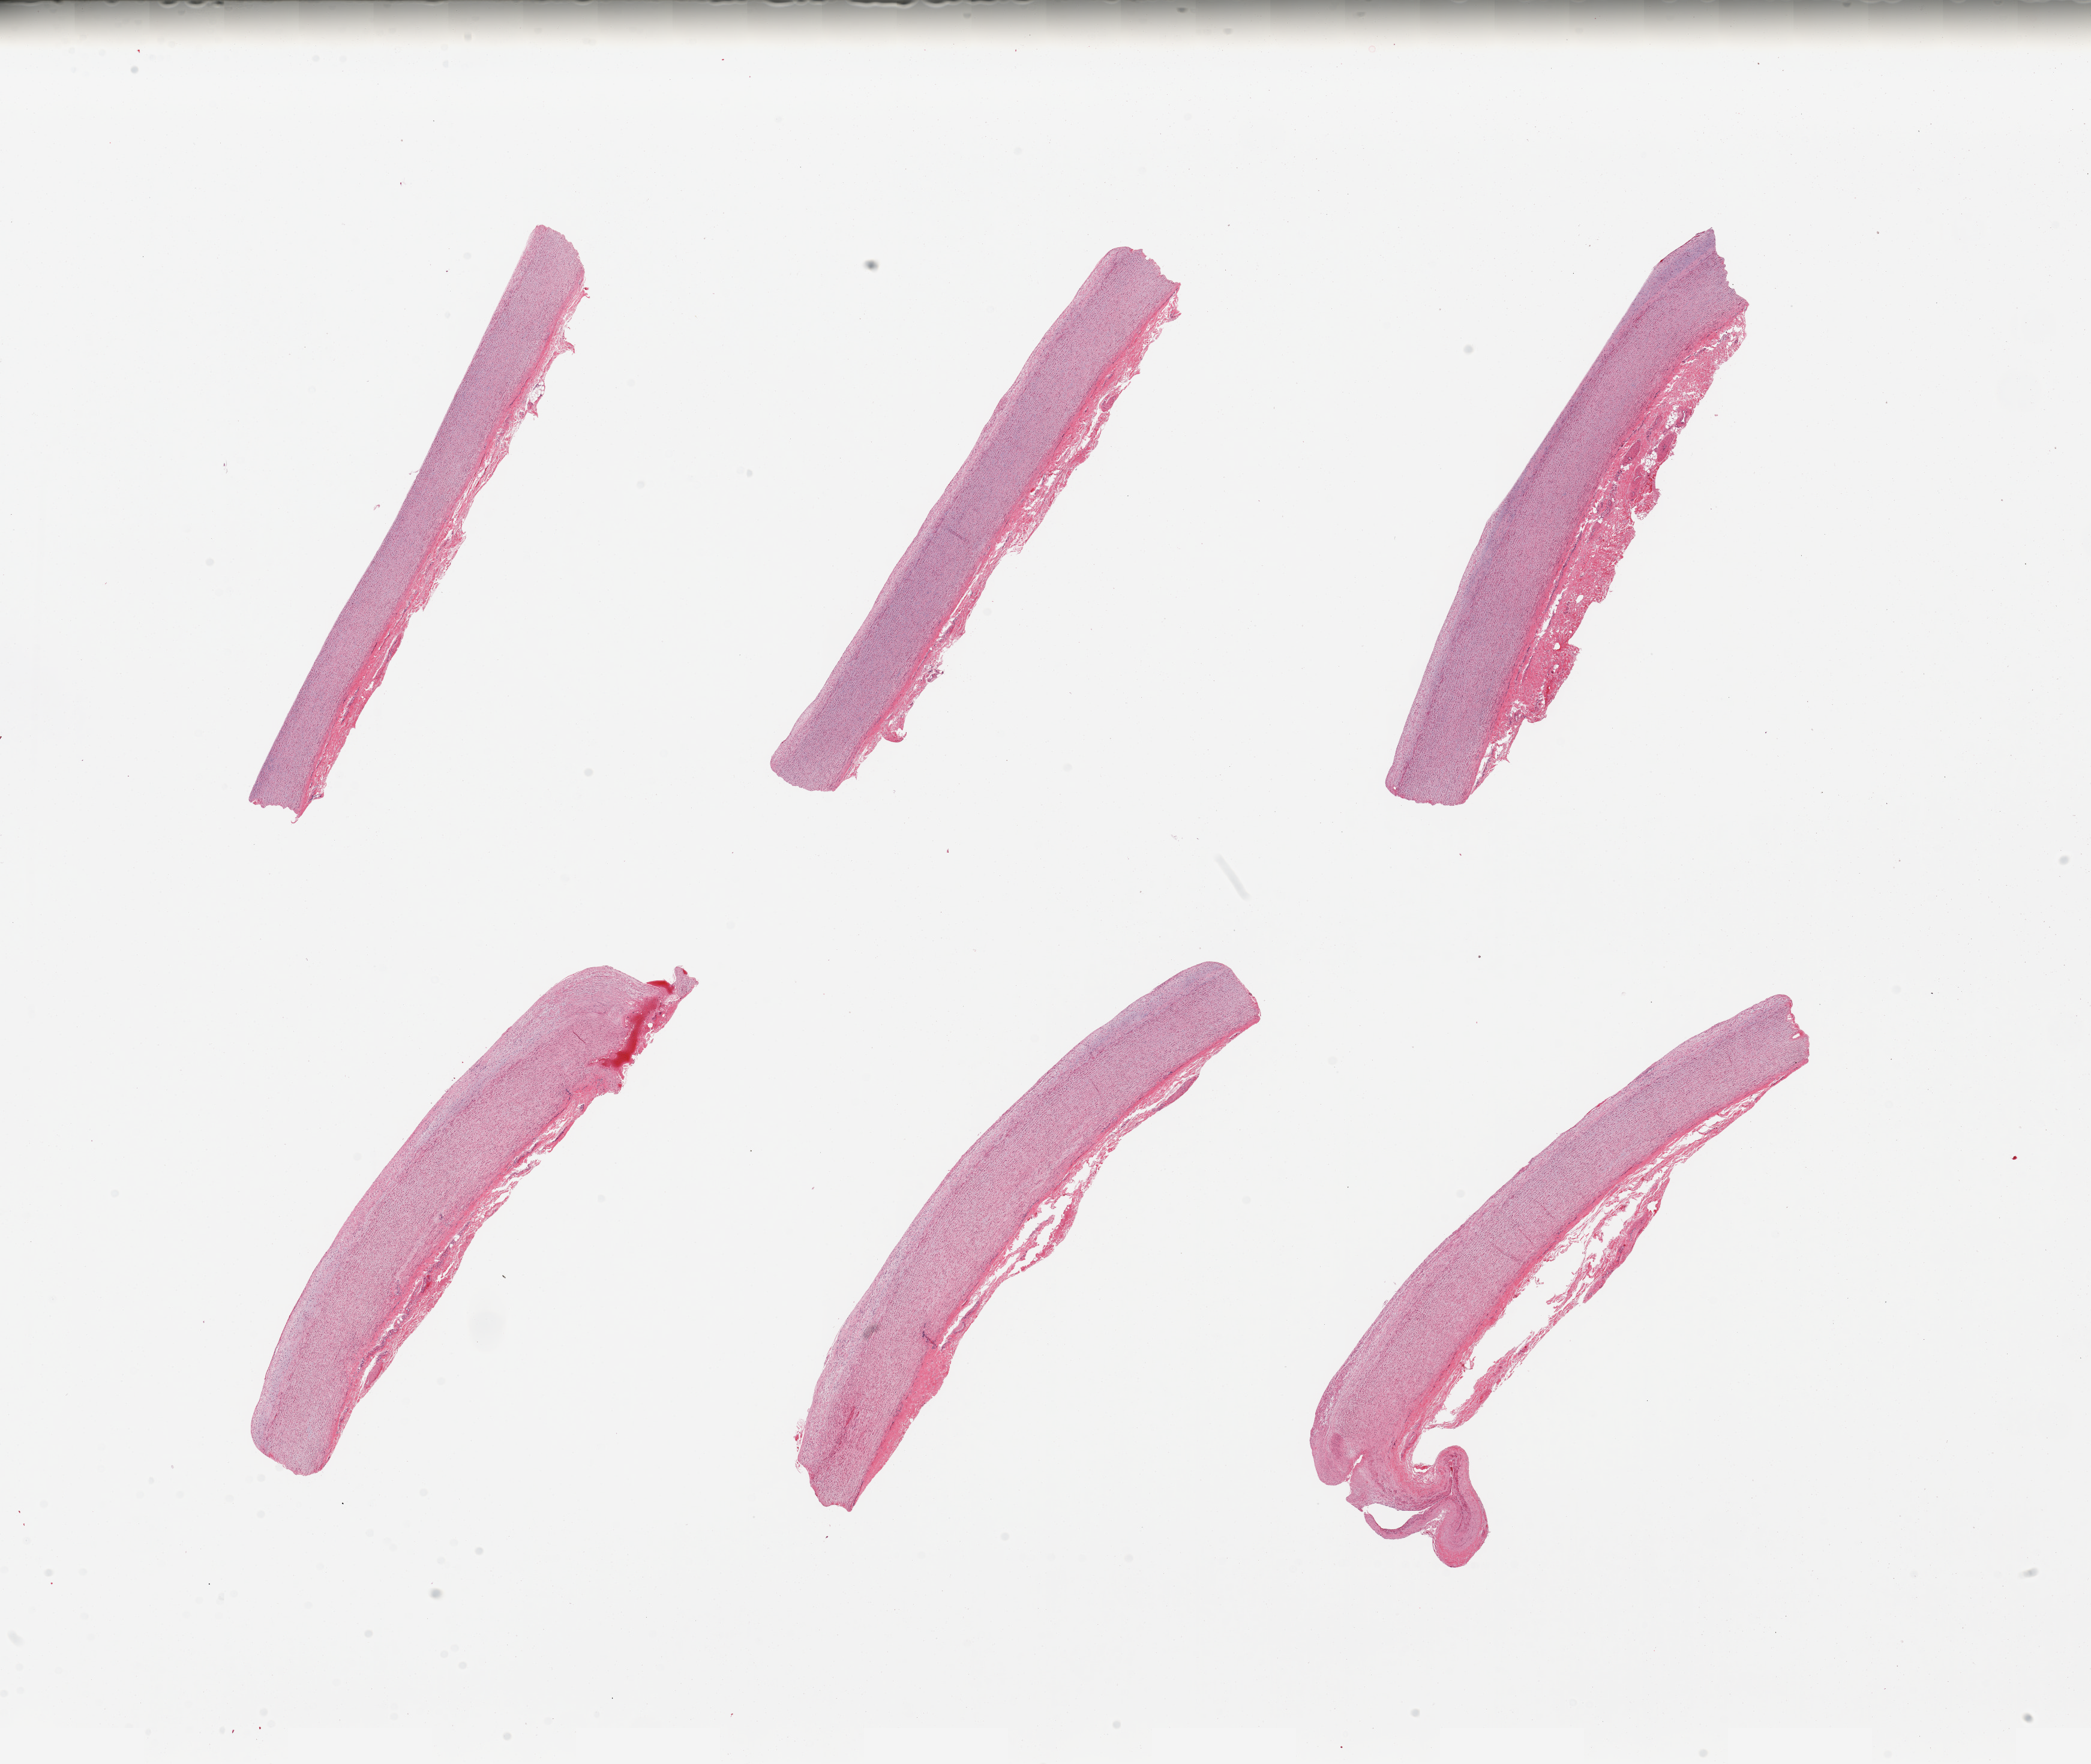
Hematoxylin and eosin (H&E) whole-slide image — shown as a low-resolution overview of the whole scanned area (about 27.6 x 23.3 mm); PAXgene-fixed, paraffin-embedded tissue; target tissue: aorta; donor tissue sample. Donor: female.
* review note (as recorded): 6 pieces ~0.5mm adherent serosa